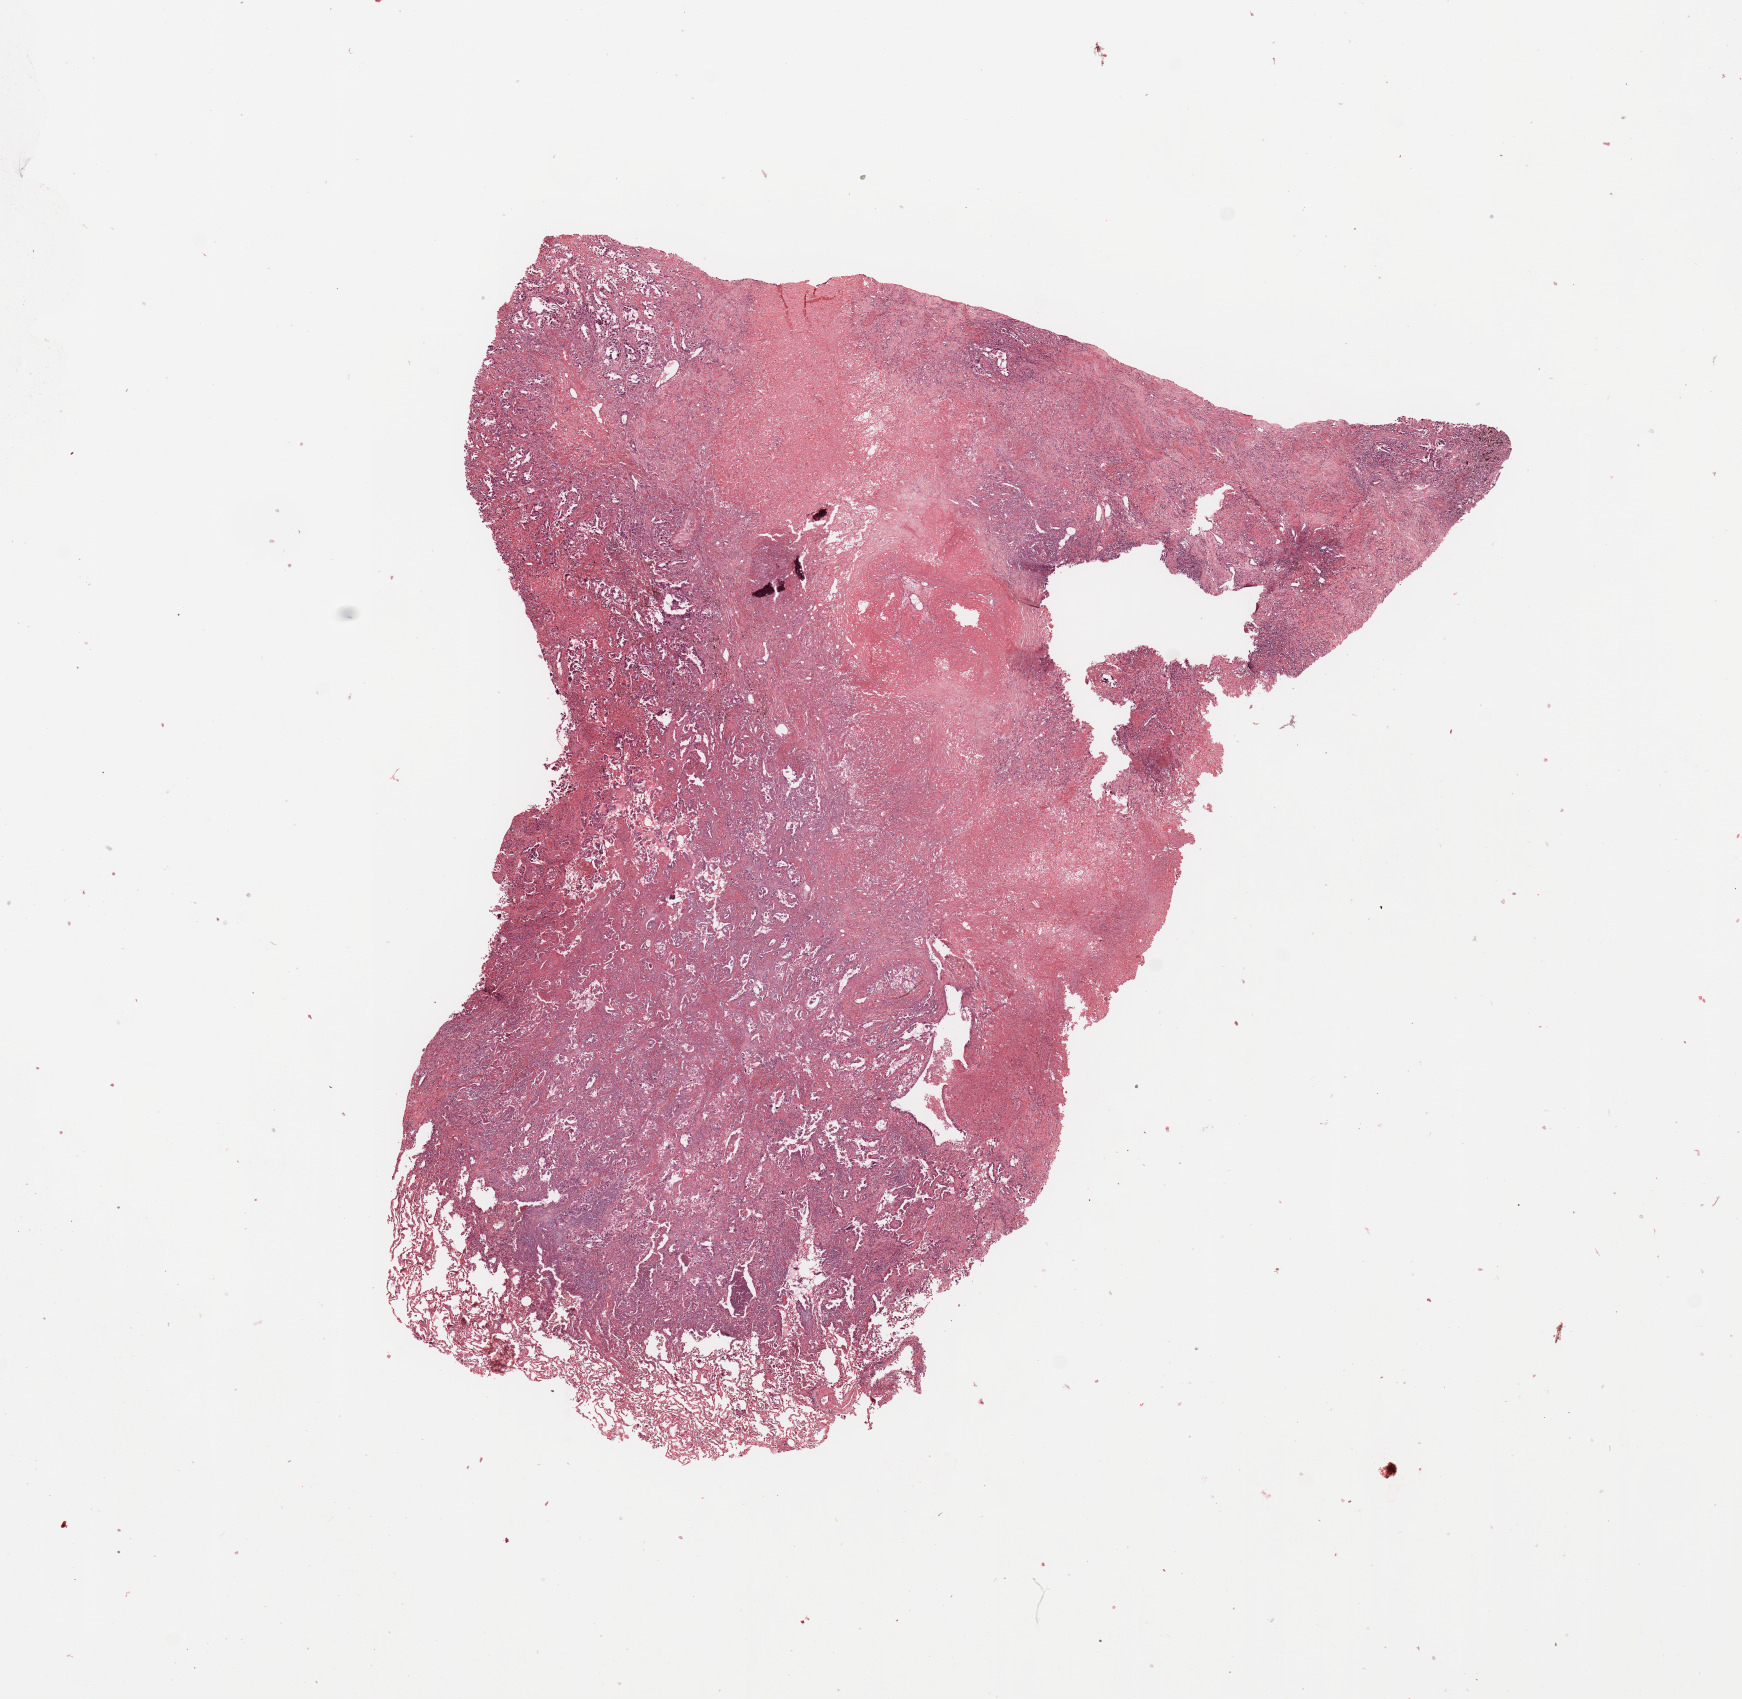
Whole-slide histology image, H&E-stained, a low-resolution overview of the entire scanned area, about 13.8 x 13.4 mm, lung, tumour tissue. Male, 63 y/o. Histologic grade: G2 (moderately differentiated).
Histologic diagnosis: Adenocarcinoma, NOS. Primary tumour site (as recorded): left upper lobe. AJCC pathologic stage: IIIA.